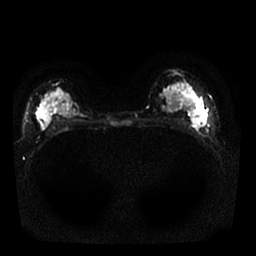
Breast MRI, one axial slice. Position 11 of 25 along the scan axis. Diffusion-weighted series; image 2 of 4 stored at this slice position (different b-values; order by instance number). 1.5 T. 4 mm slice thickness. 256 × 256 image matrix. Female patient.
Annotated regions visible in this slice (expert manual segmentation):
- tumour on diffusion-weighted imaging: box from (x=192, y=116) to (x=204, y=127) px